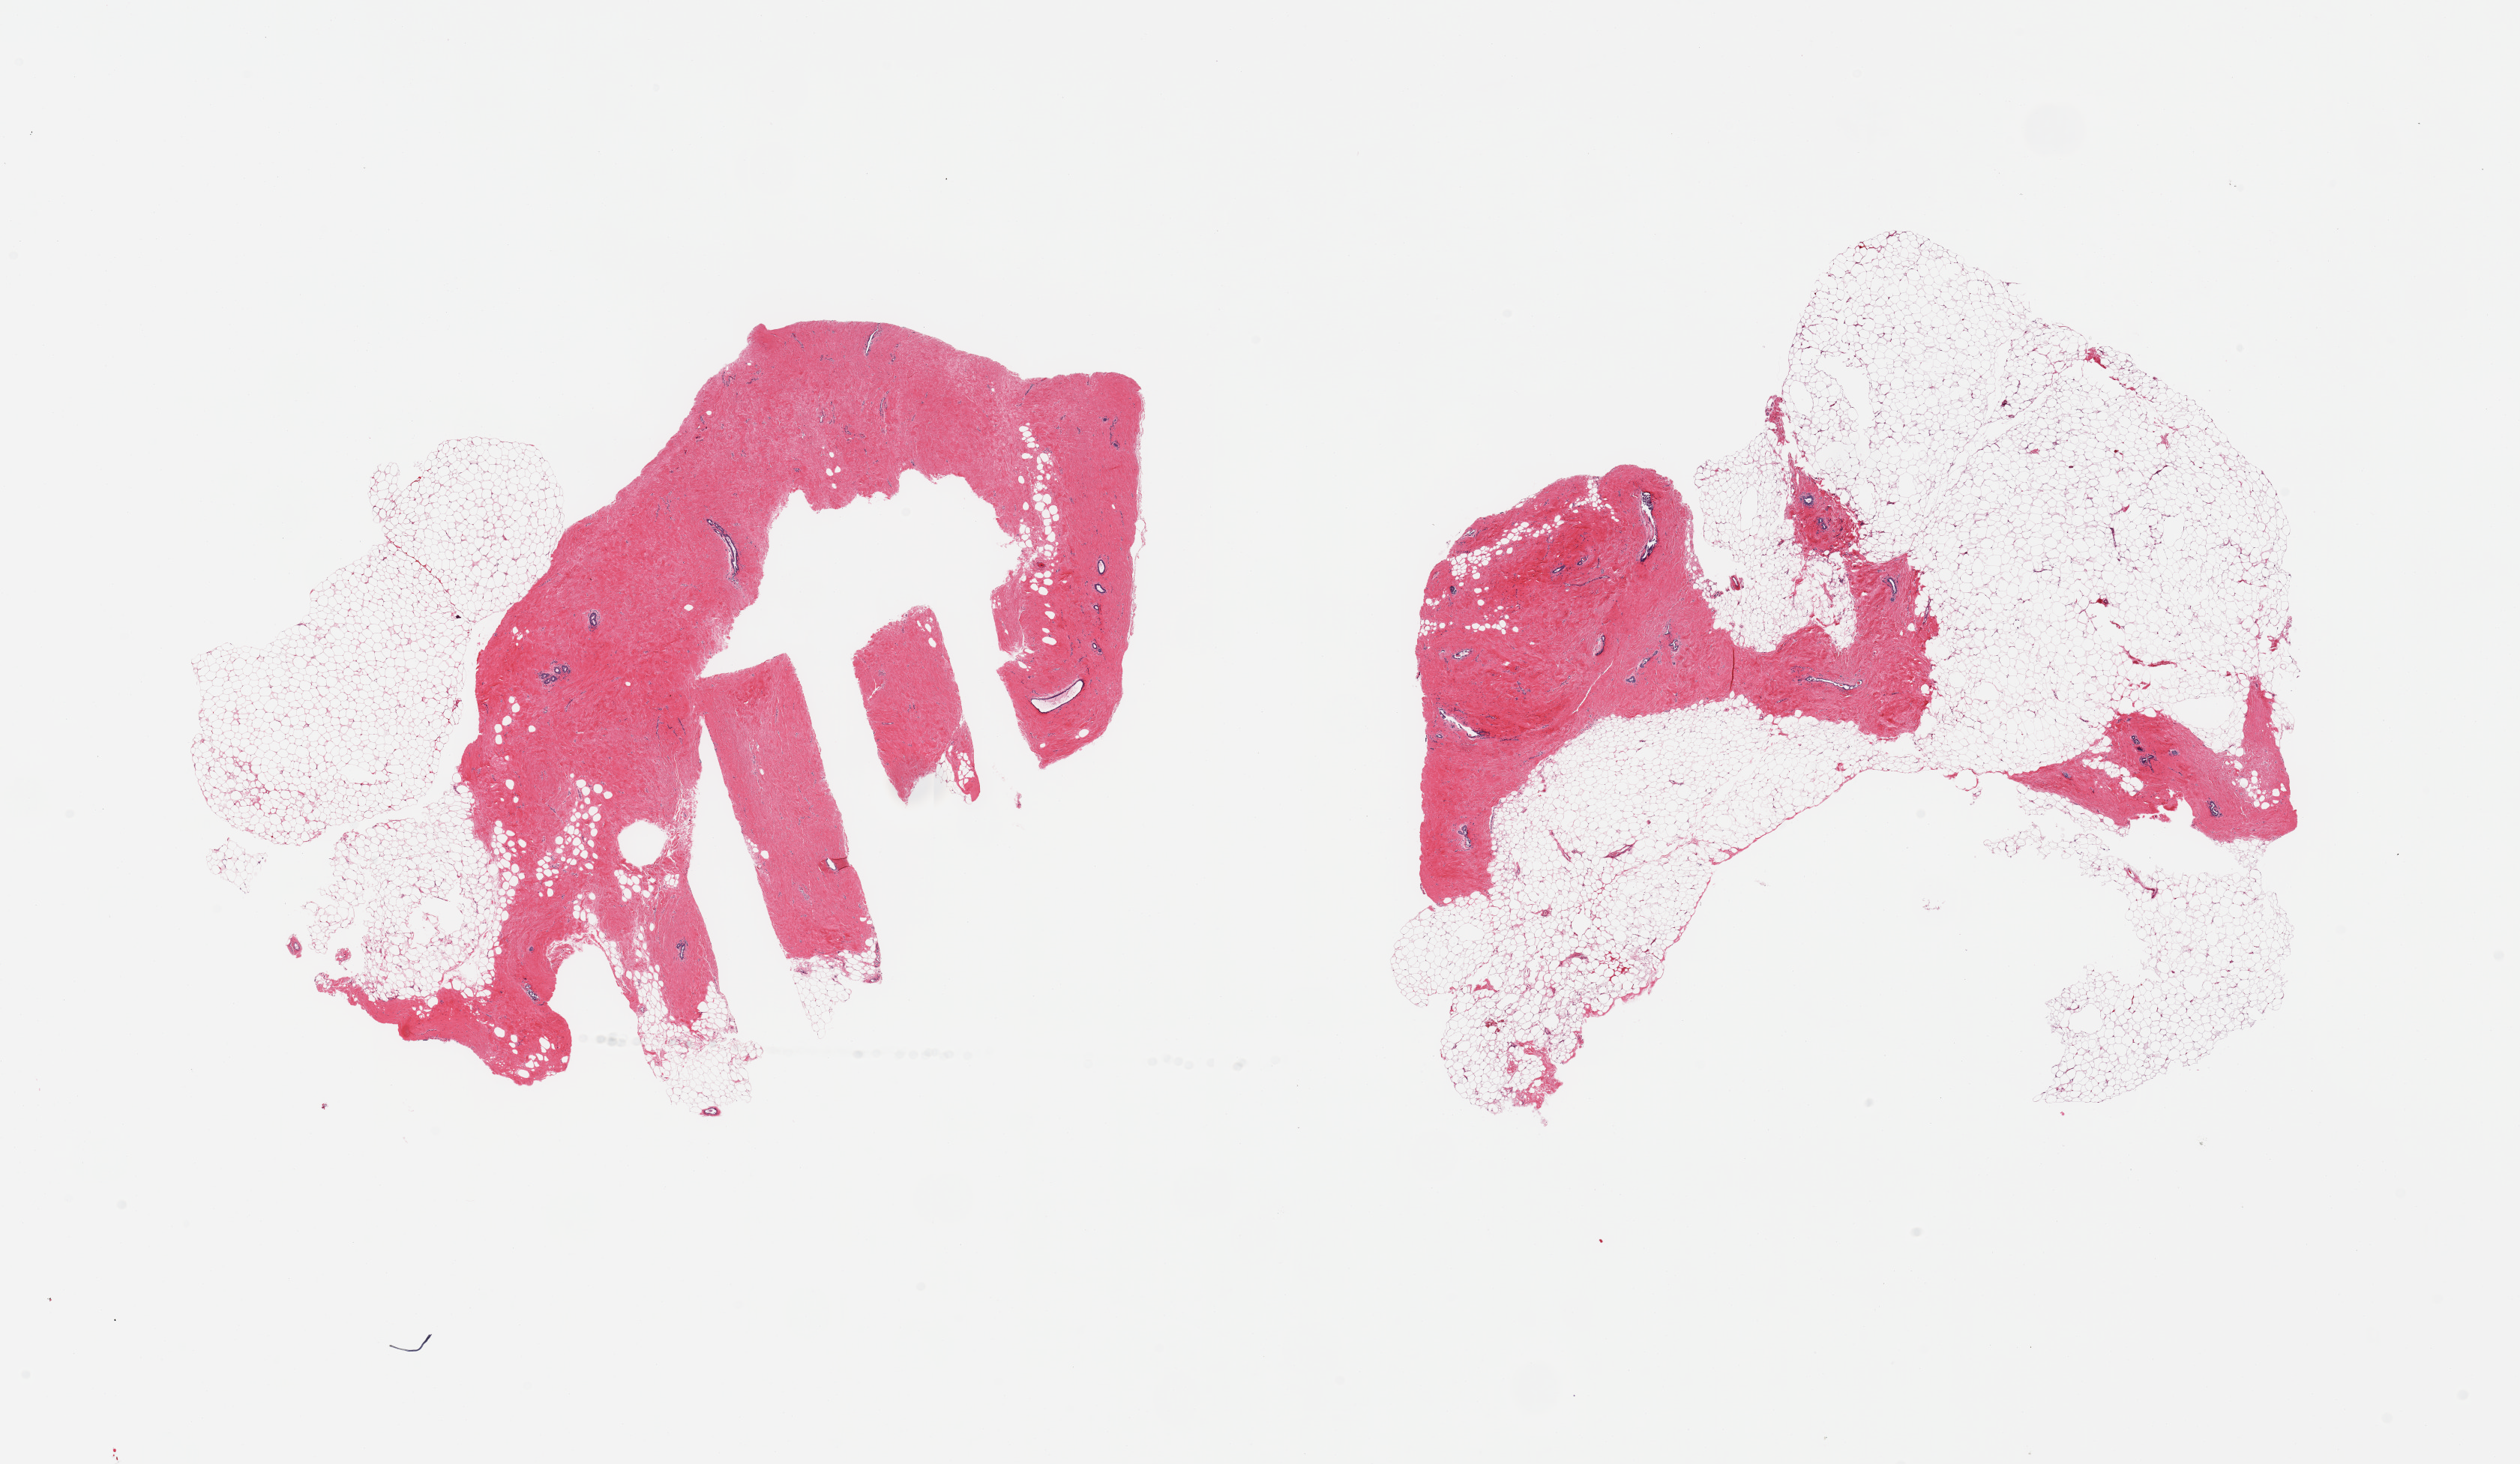
Whole-slide image, H&E stain, brightfield, low-resolution overview of the scanned area, about 26.6 x 15.4 mm (from a 20x scan); PAXgene-fixed paraffin-embedded (PFPE) section; section of breast (target tissue); donor tissue sample.
Review note (as recorded): 2 pieces; ducts and fibrosis consistent with gynecomastoid hyperplasia; 50% fat.